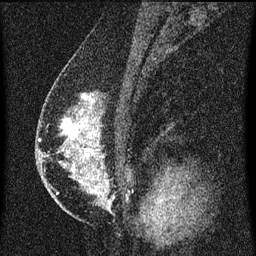
Breast MRI (dynamic contrast-enhanced), one sagittal slice; position 36 of 60 along the scan axis; dynamic contrast-enhanced series, image 2 of 3 at this slice position (ordered by acquisition); 1.5 T; TE 4.2 ms, TR 8 ms; 2 mm slice thickness; 256 × 256 image matrix. Female patient, age 47 years.
Annotated regions visible in this slice (semi-automatically segmented with operator editing):
- analysis volume of interest (the breast-tissue region the enhancement analysis was run in; not a lesion): bounding box <50,80,131,203> (left, top, right, bottom; pixels)
- tumour enhancement mask (voxels above the 70 % enhancement threshold inside the analysis volume of interest): <63,96,108,193>